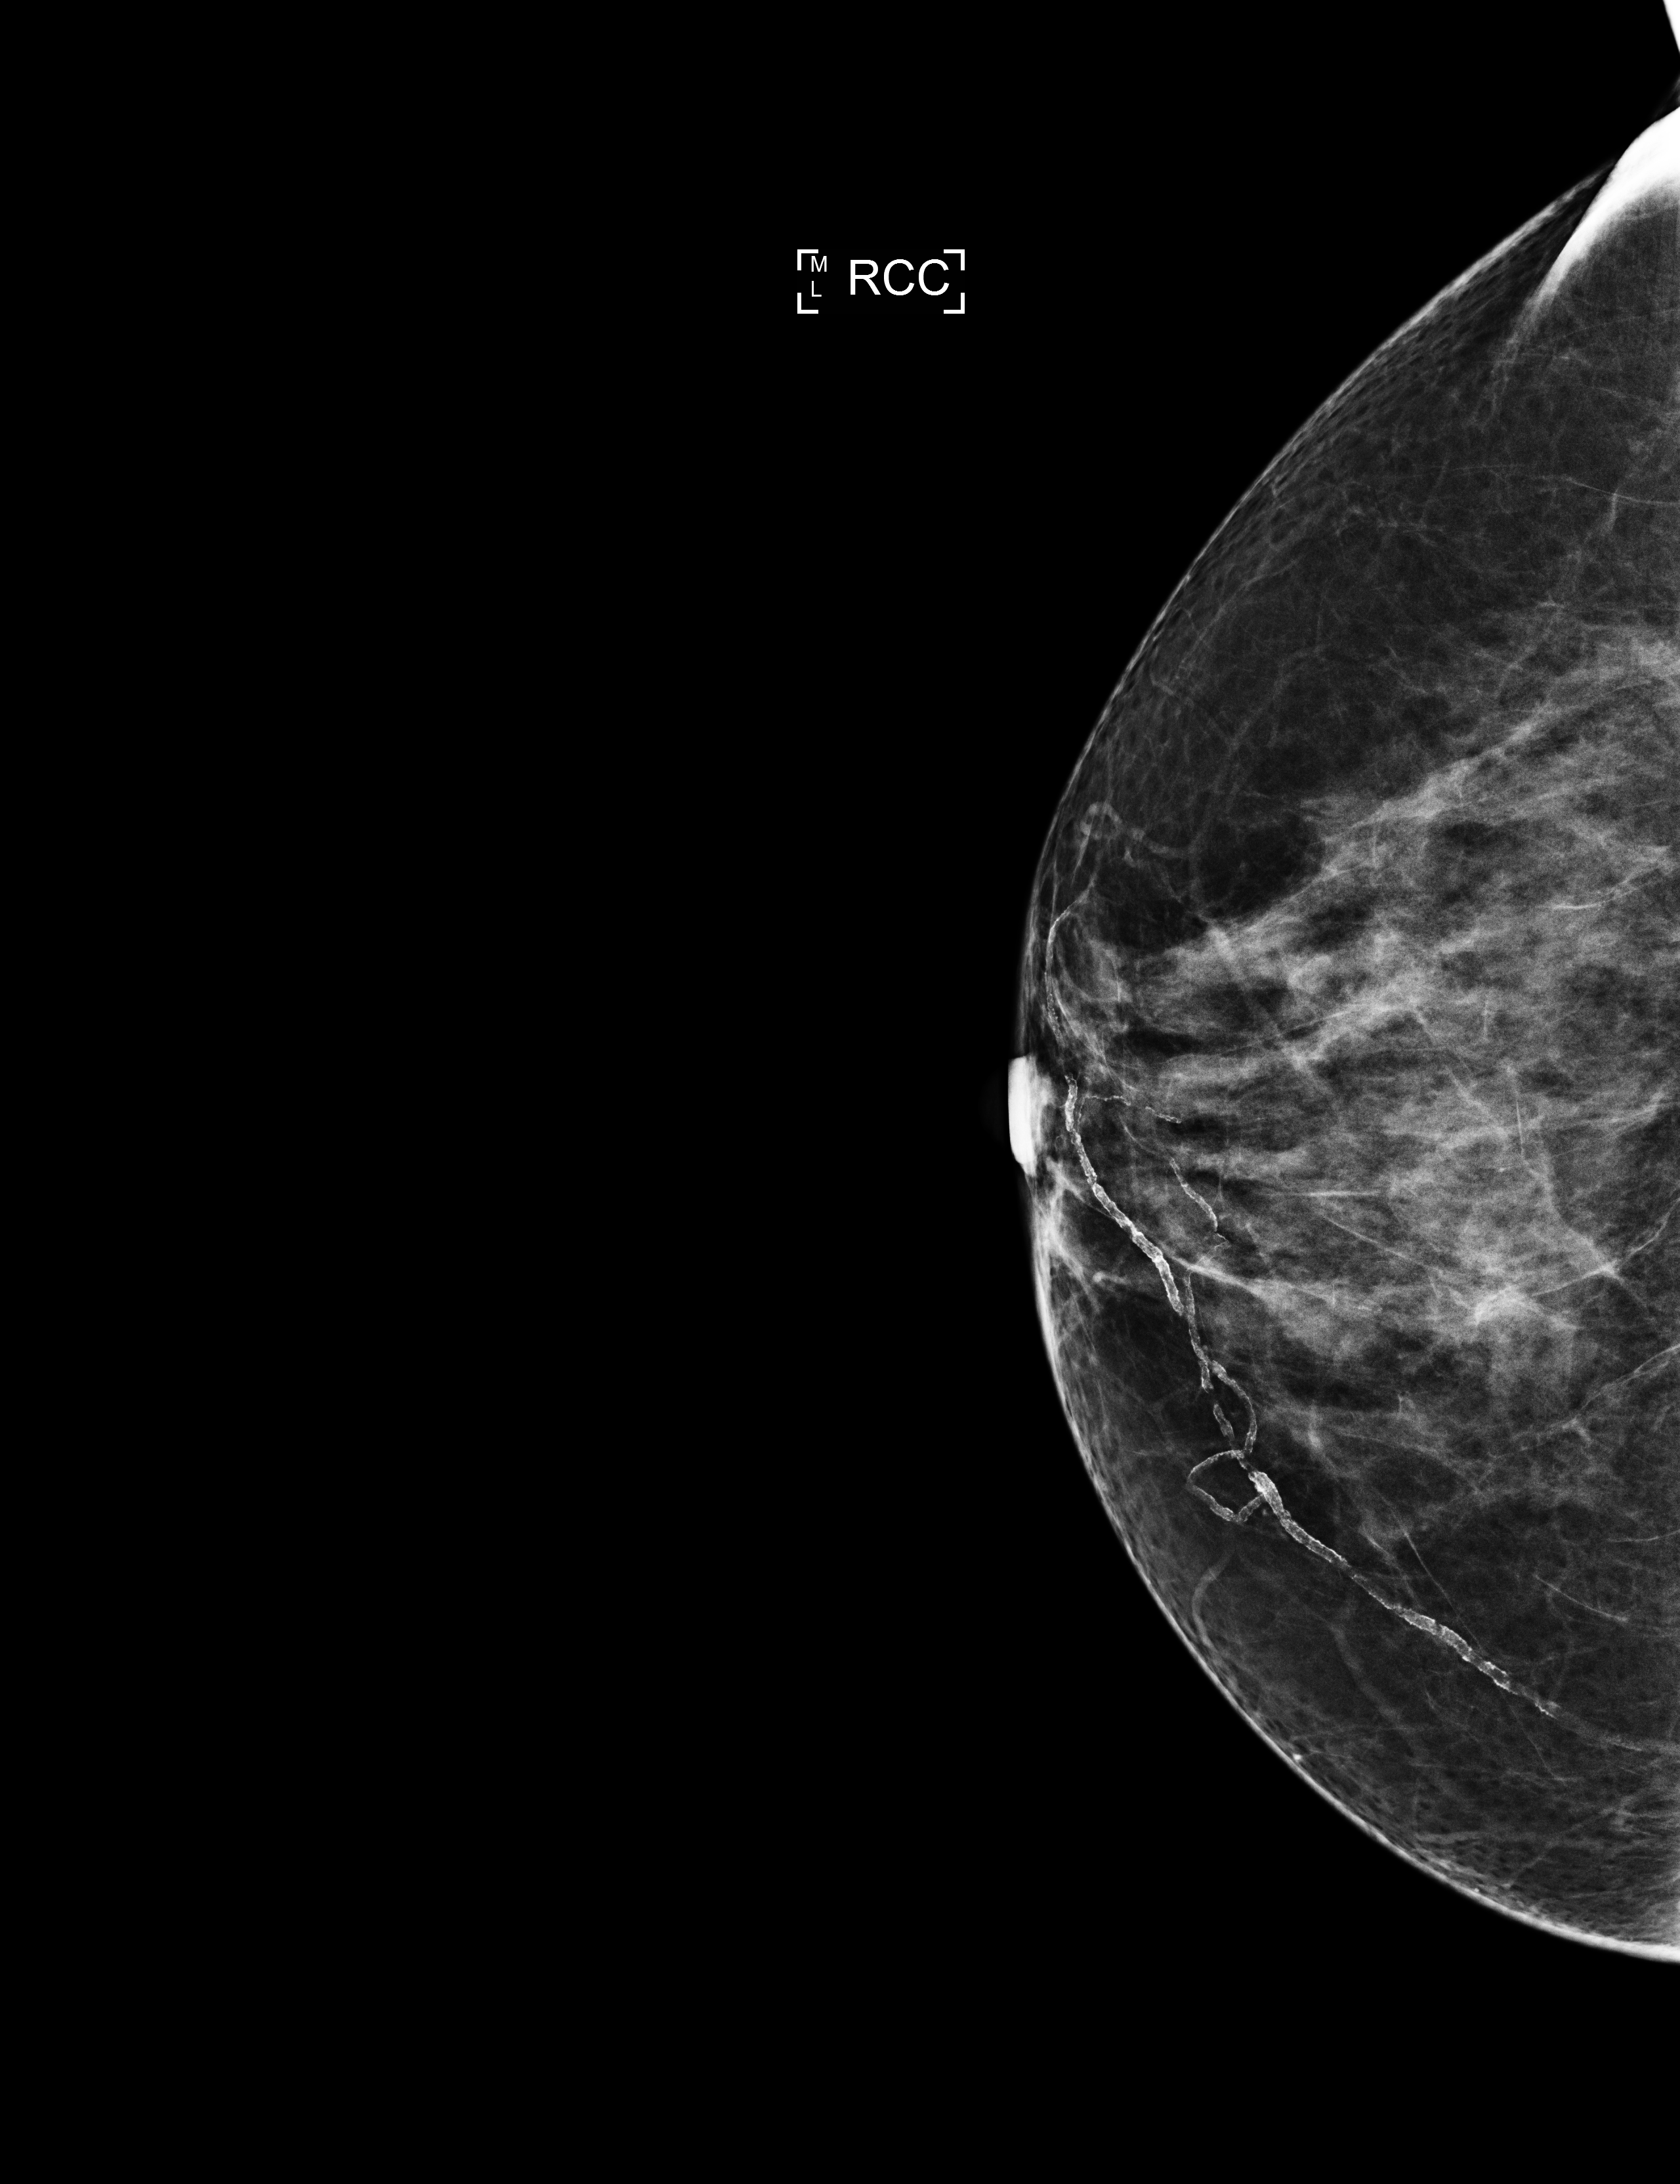
Screening examination. Patient aged 60 years (female).
Image type: full-field digital mammogram. Breast: right. Projection: CC view.